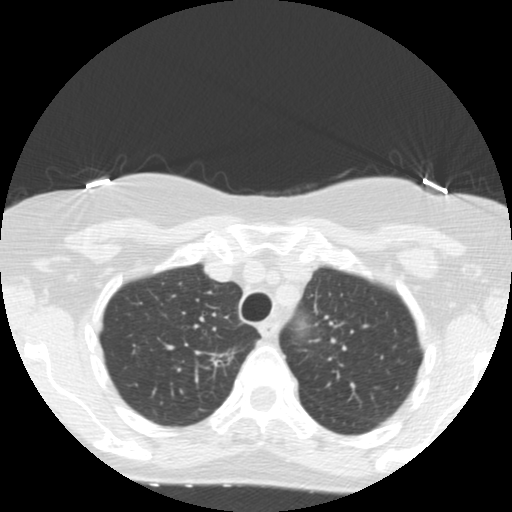
Chest CT (low-dose screening protocol), one axial image; baseline annual screen; lung window (W 1500 / L -600 HU); 2.5 mm slice thickness; 120 kVp. Female, age 67 years at enrolment.
- Lesion marked by an expert reader, bounding box (x1, y1, x2, y2) in pixels: (194, 340, 254, 386).
- Screening reader's record for this exam (one nodule recorded; not confirmed to be the boxed lesion): non-calcified nodule or mass ≥4 mm, right upper lobe, 16 × 7 mm, poorly defined margins, mixed attenuation.
- Lung cancer was diagnosed 132 days after this screen: adenocarcinoma, NOS, right upper lobe, moderately differentiated (G2), stage IA (AJCC 6th edition), 13 mm at pathology.